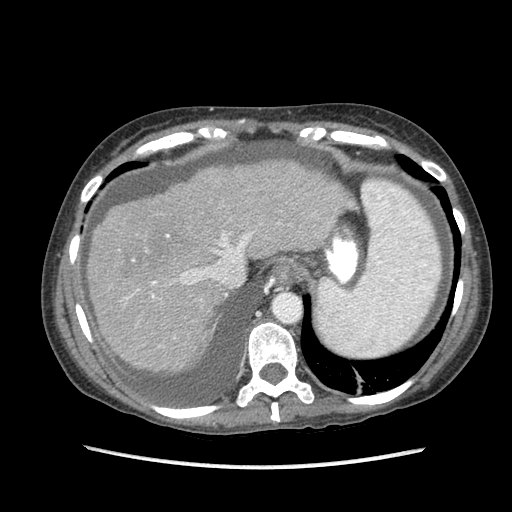
Contrast-enhanced abdominal CT (liver protocol), one axial slice; position 72 of 87 along the scan axis; reconstruction kernel STANDARD; 120 kVp; soft-tissue window (W 400 / L 40 HU); 2.5 mm slice thickness; 512 × 512 image matrix. From the clinical record (not read from this slice): diagnosis: hepatocellular carcinoma (patient treated with transarterial chemoembolisation; whether this scan precedes or follows treatment is not stated here); TNM stage (as recorded): Stage-IIIB; Child-Pugh class: A; tumour differentiation: no biopsy; tumour nodularity: uninodular.
Structures marked on this image (semi-automatic segmentation, software-assisted and operator-edited):
- liver parenchyma outside the tumour (the mass and vessels are separate outlines, so this box may not span the whole liver): box from (x=88, y=160) to (x=350, y=370) px
- liver vessels: (x=125, y=232)–(x=254, y=300)